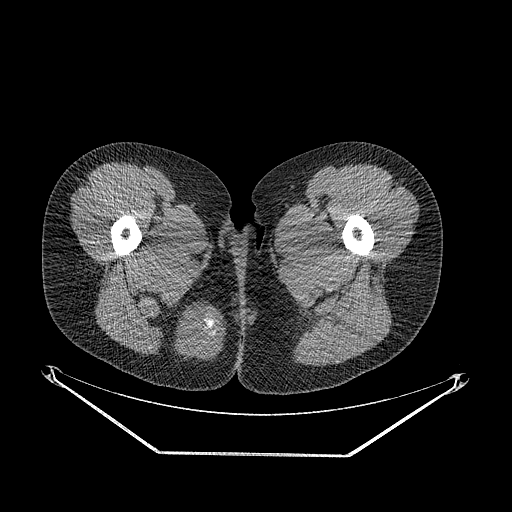
CT of an extremity soft-tissue mass (from a PET/CT study), one axial slice. Position 25 of 267 along the scan axis. 120 kVp. Soft-tissue window (W 400 / L 40 HU). 3.75 mm slice thickness. 512 × 512 image matrix, field of view 500 × 500 mm. Female patient. From the clinical record (not read from this slice): histological type: epithelioid sarcoma; grade: intermediate; site of the primary tumour: right buttock.
Outlined on this slice (expert contour drawn on MRI and transferred to this co-registered scan by the dataset authors):
- gross tumour volume including surrounding oedema: box from (x=171, y=301) to (x=225, y=362) px
- gross tumour volume (mass): (x=174, y=306)–(x=225, y=359)